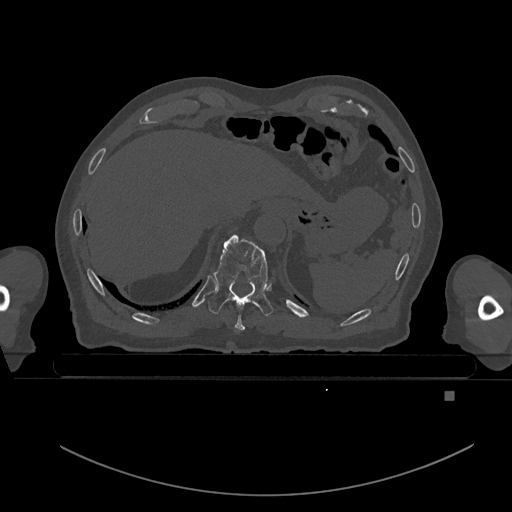
CT including the spine, one axial slice; position 96 of 969 along the scan axis; bone window (W 1800 / L 400 HU); 0.5 mm slice thickness; 512 × 512 image matrix, field of view 456 × 456 mm. Male patient, age 82 years. From the clinical record (not read from this slice): primary cancer: prostate; vertebrae with lytic lesions (as recorded): T11, T9, T8, T2.
Annotated regions visible in this slice (semi-automatically segmented with operator editing):
- T10 vertebra: box from (x=208, y=234) to (x=274, y=317) px
- T9 vertebra: (x=235, y=315)–(x=245, y=331)